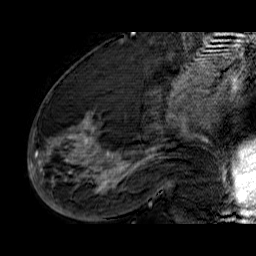
Breast MRI (dynamic contrast-enhanced), one sagittal slice; position 31 of 60 along the scan axis; dynamic contrast-enhanced series, time point 2 of 6 at this slice position (early post-contrast); 1.5 T; TE 6.5 ms, TR 32.9 ms; 4 mm slice thickness; 256 × 256 image matrix. Female patient. From the clinical record (not read from this slice): setting: breast cancer imaged before/during neoadjuvant chemotherapy; receptor status: HR-positive, HER2-negative.
Structures marked on this image (semi-automatic segmentation, software-assisted and operator-edited):
- analysis volume of interest (the breast-tissue region the enhancement analysis was run in; not a lesion): bounding box (x1, y1, x2, y2) in pixels: (33, 74, 176, 210)
- tumour enhancement mask (voxels above the 100 % enhancement threshold inside the analysis volume of interest): (33, 114, 152, 194)